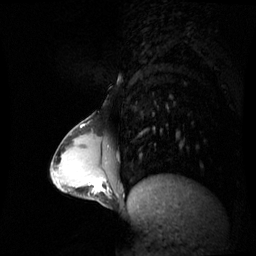
Breast MRI (dynamic contrast-enhanced), one sagittal slice. Position 21 of 60 along the scan axis. Dynamic contrast-enhanced series, image 2 of 3 at this slice position (ordered by acquisition). 1.5 T. TE 4.2 ms, TR 8.9 ms. 2.4 mm slice thickness. 256 × 256 image matrix, field of view 300 × 300 mm. Female patient, age 34 years. Case-level facts recorded for this patient, not image findings: setting: breast cancer imaged before/during neoadjuvant chemotherapy; receptor status: triple-negative.
Annotated regions visible in this slice (semi-automatic segmentation, software-assisted and operator-edited):
- analysis volume of interest (the breast-tissue region the enhancement analysis was run in; not a lesion): bounding box [x1, y1, x2, y2] px = [65, 168, 106, 203]
- tumour enhancement mask (voxels above the 70 % enhancement threshold inside the analysis volume of interest): [93, 178, 102, 191]